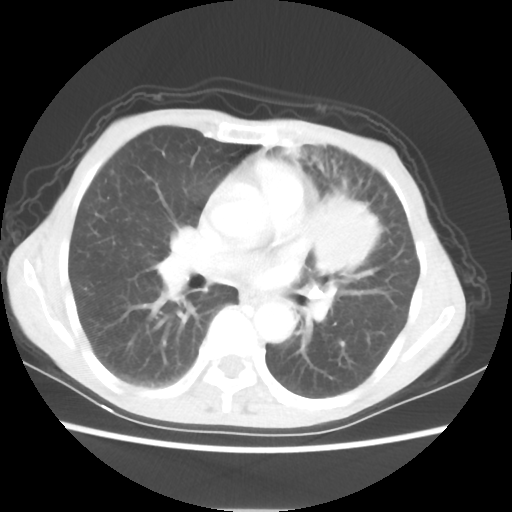
Chest CT, one axial slice; slice 32 of 56 in the series (ordered by position); lung window (W 1500 / L -600 HU); 512 × 512 image matrix, field of view 331 × 331 mm. Female patient, age 60 years. From the clinical record (not read from this slice): clinical TNM (as recorded): T4 N1 M0.
Annotated regions visible in this slice (bounding box drawn by a radiologist):
- lung tumour (recorded histology: adenocarcinoma): bounding box (x1, y1, x2, y2) in pixels: (311, 191, 385, 283)